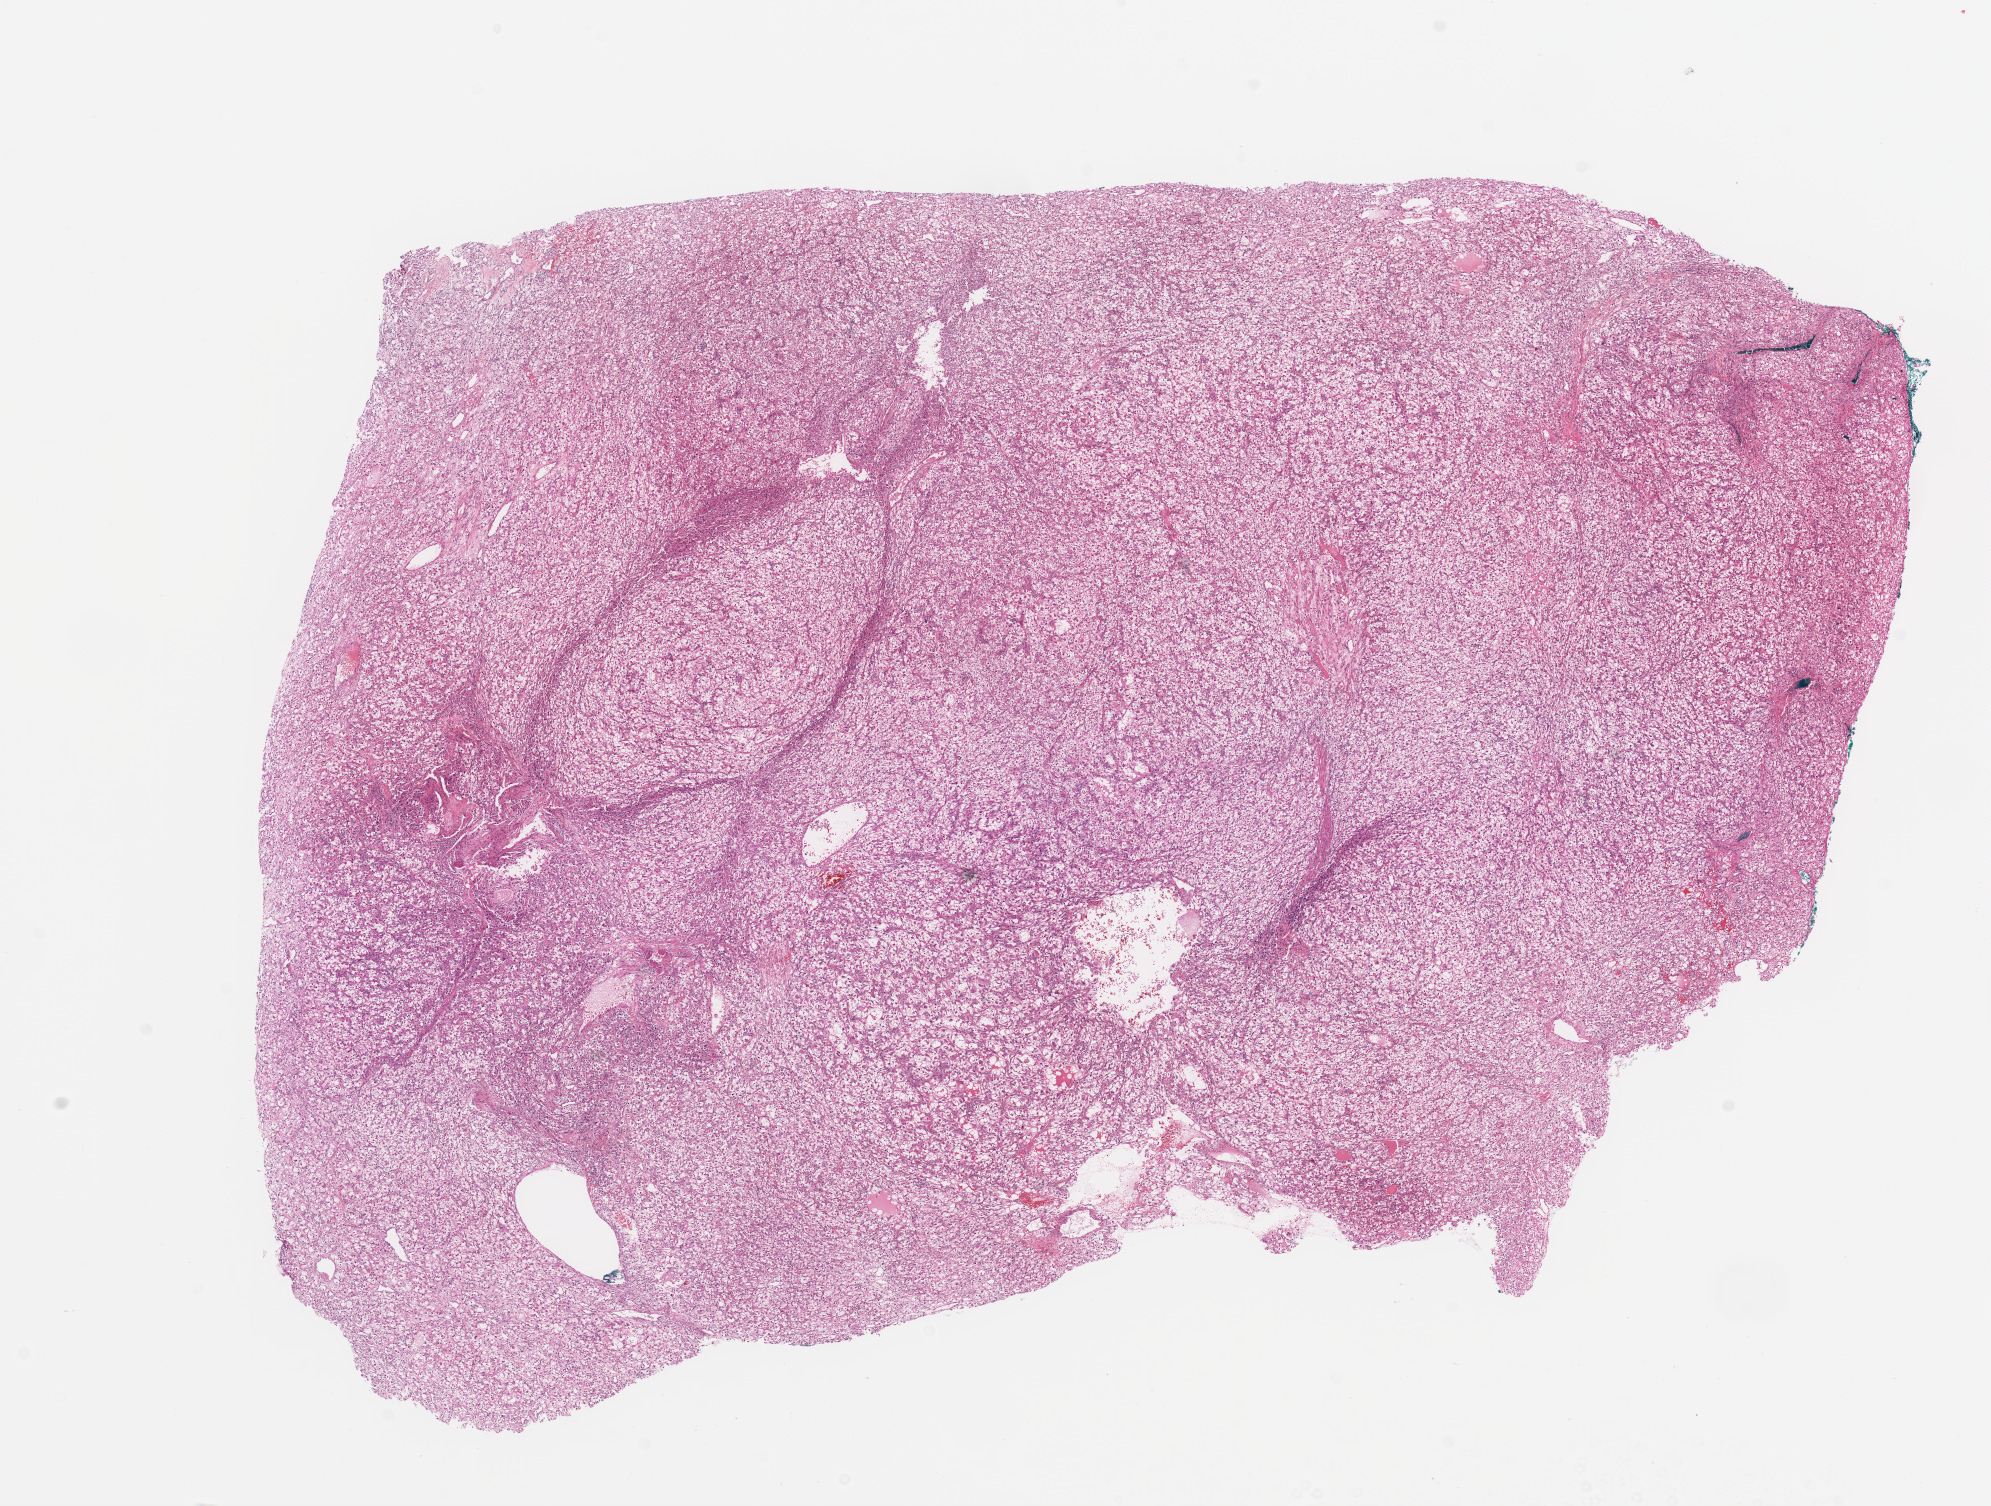
H&E-stained whole-slide image, low-resolution overview of the scanned area, about 15.8 x 11.9 mm. Tumour tissue sample, sampled site: kidney. Patient: male, age 70 years. Histologic grade: G3 (poorly differentiated). Pathologist review of this section (percent, as recorded): tumour nuclei 85%, necrosis 5%.
AJCC pathologic stage: II. Primary tumour site (as recorded): middle. Histologic diagnosis: Renal cell carcinoma, NOS.